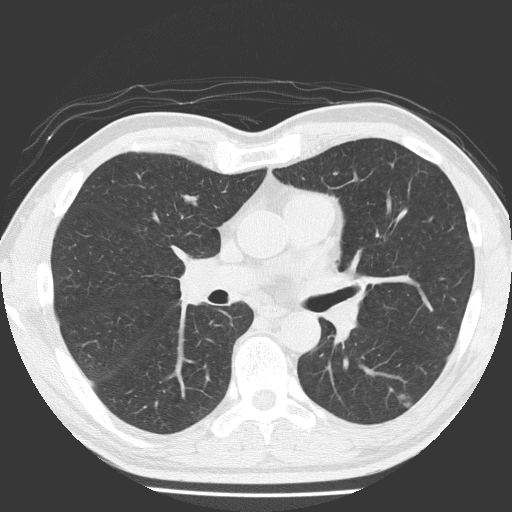
Low-dose screening chest CT, one axial slice. Slice 103 of 184 in the series (ordered by position). 120 kVp. Lung window (W 1500 / L -600 HU). 2 mm slice thickness. 512 × 512 image matrix, field of view 348 × 348 mm.
Structures marked on this image (outlined manually by an expert reader):
- lesion 1 (tumor, lower lobe of left lung): box from (x=391, y=391) to (x=410, y=407) px